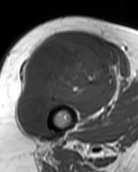
MRI of an extremity soft-tissue mass, one axial slice; position 66 of 99 along the scan axis; MR volume resampled by the dataset authors to the PET/CT grid (not the native acquisition matrix); 138 × 172 image matrix, field of view 135 × 168 mm. Female patient. From the clinical record (not read from this slice): histological type: pleiomorphic undifferentiated sarcoma; grade: high; site of the primary tumour: right quadricep.
Outlined on this slice (expert contour drawn on MRI and transferred to this co-registered scan by the dataset authors):
- gross tumour volume including surrounding oedema: bounding box (x1, y1, x2, y2) in pixels: (18, 38, 109, 126)
- gross tumour volume (mass): (18, 38, 109, 126)